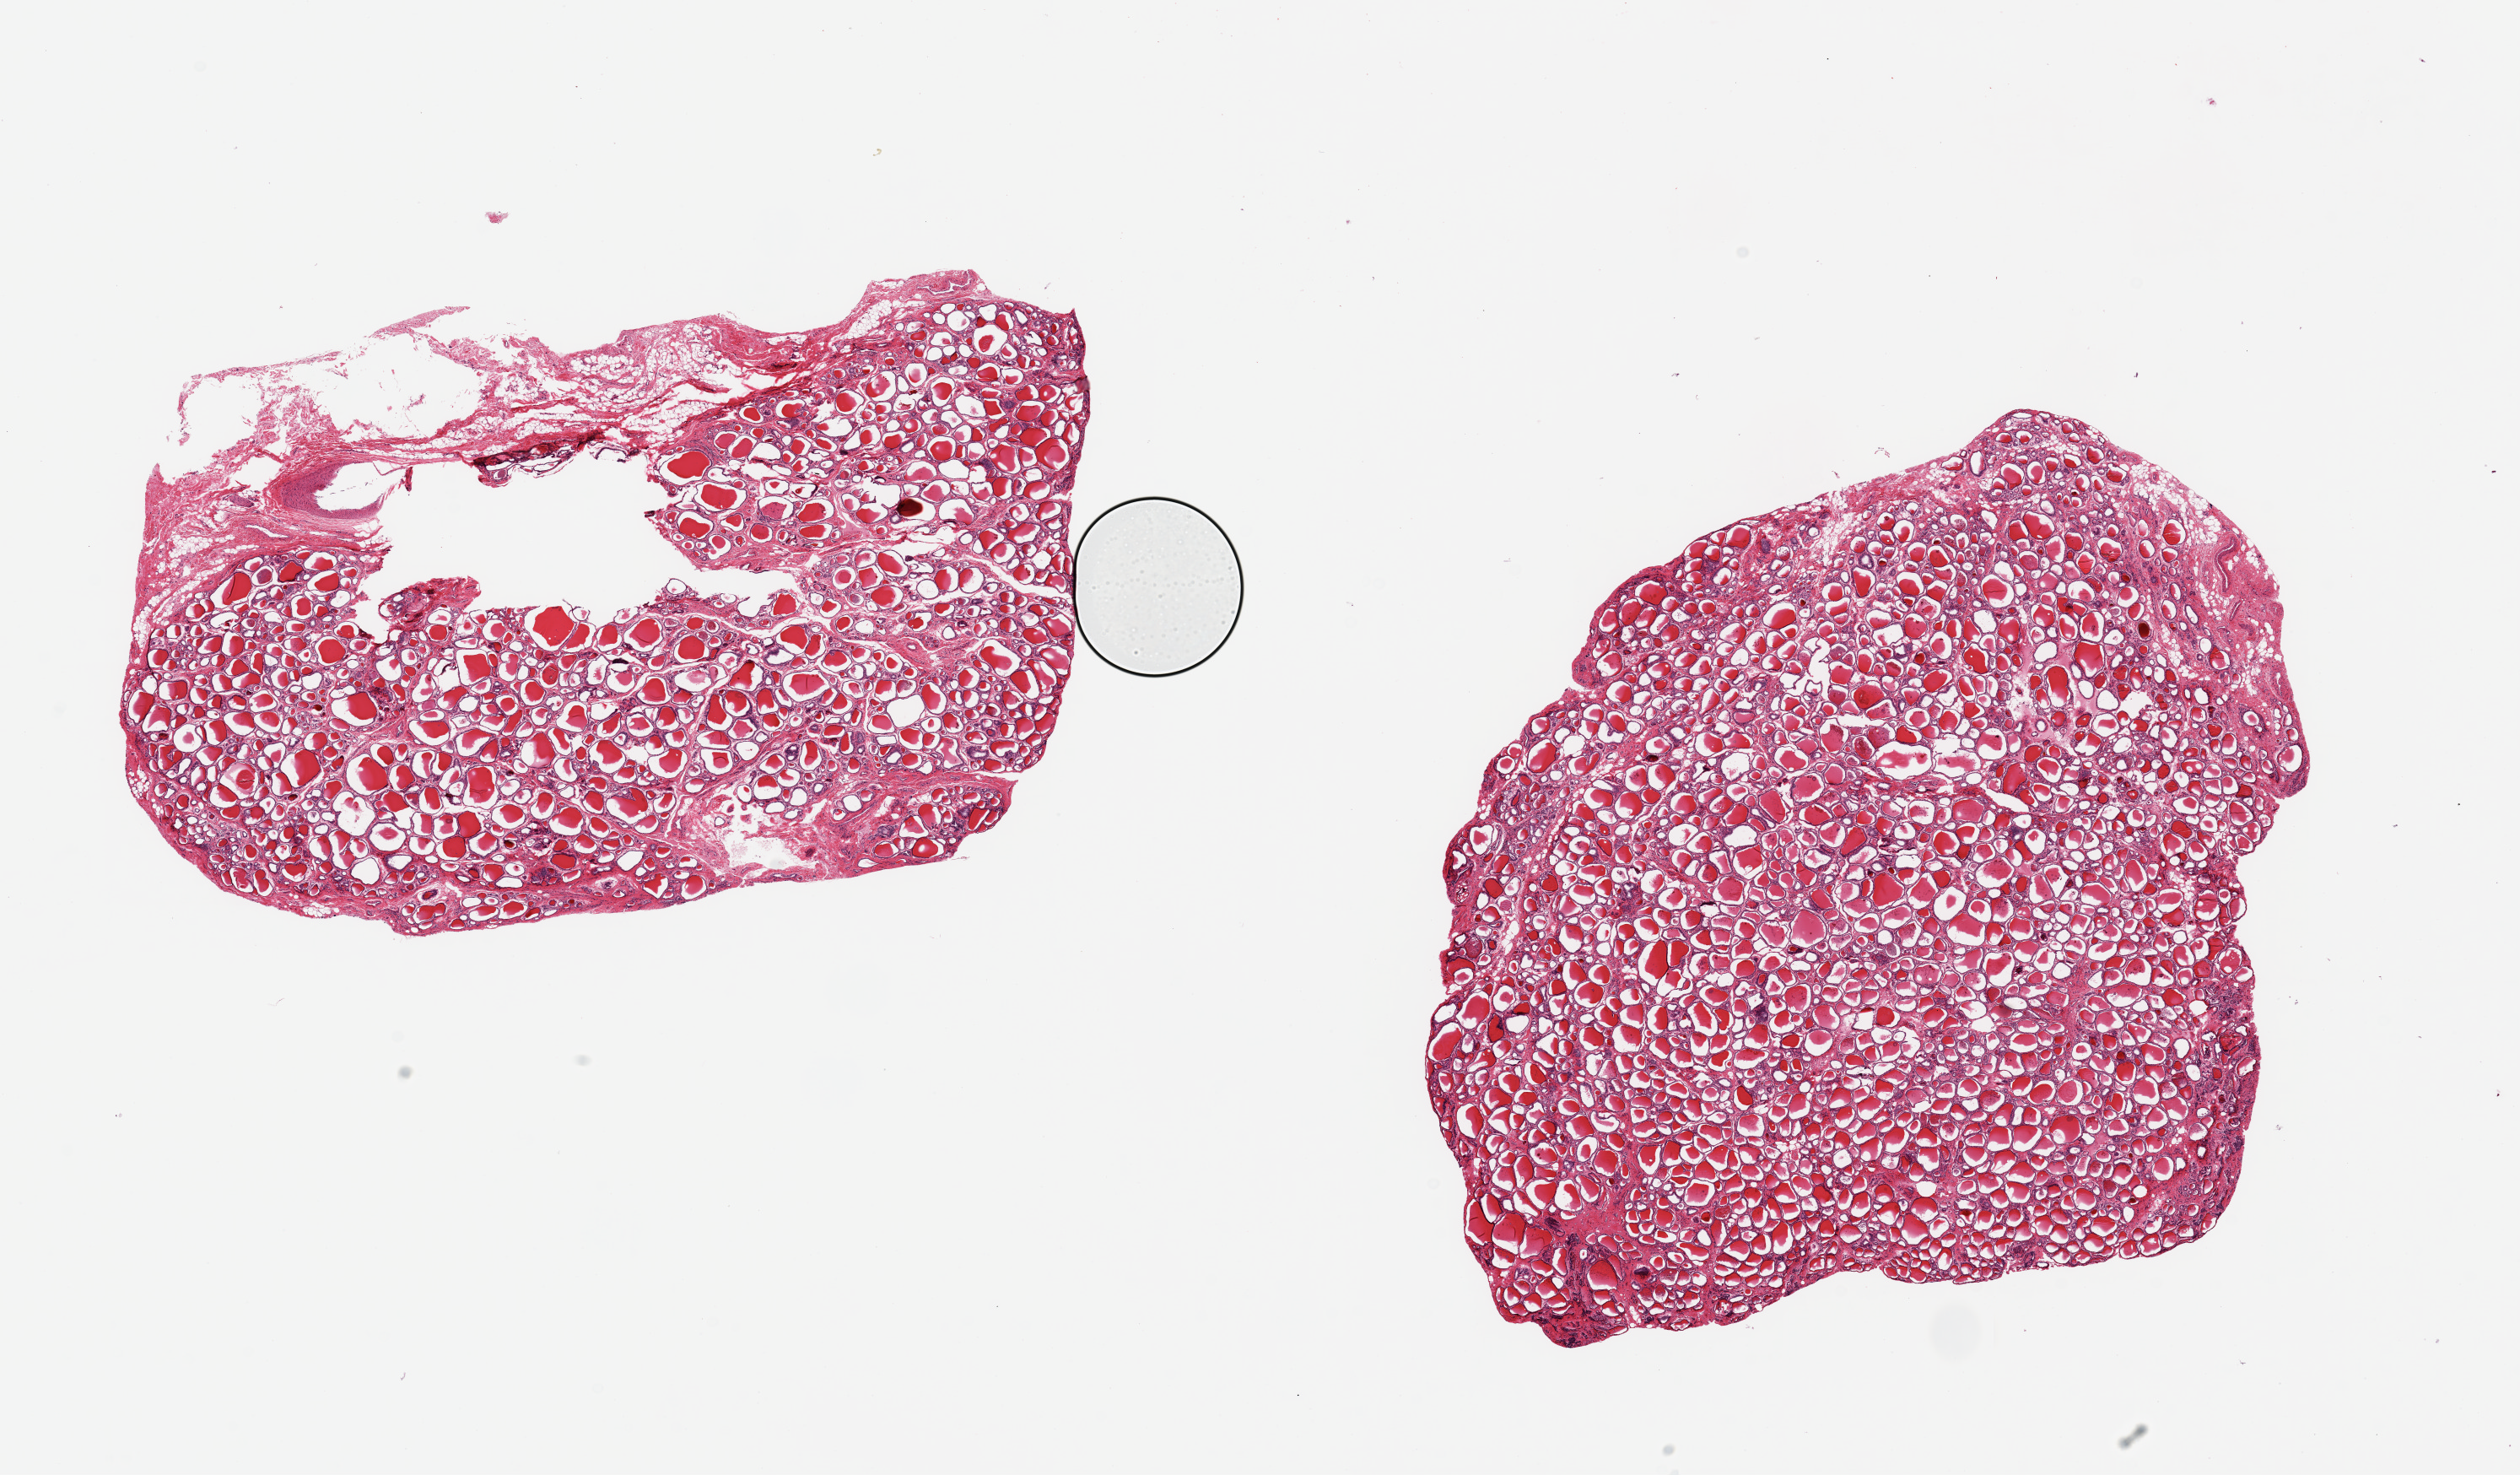
Whole-slide image, hematoxylin and eosin (H&E) stain, brightfield, a low-resolution overview of the entire scanned area, about 23.6 x 13.8 mm (from a 20x scan), PAXgene-fixed, paraffin-embedded tissue, section of thyroid (target tissue), donor tissue sample.
Reviewer comment on this tissue sample: 2 pieces ~9x7mm.